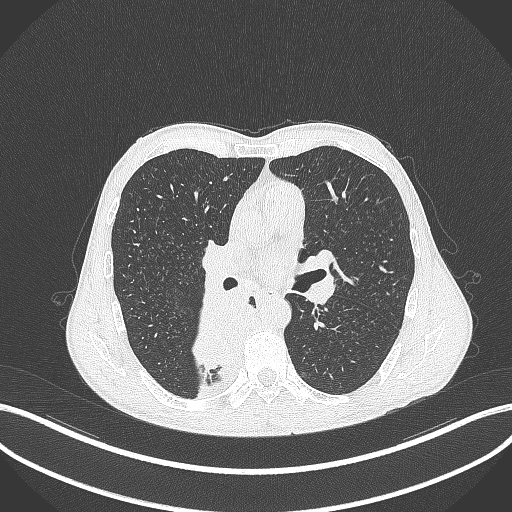
Chest CT, one axial slice. Slice 211 of 371 in the series (ordered by position). Reconstruction kernel B70f. 120 kVp. Lung window (W 1500 / L -600 HU). 512 × 512 image matrix, field of view 400 × 400 mm. Patient: male, 58 years. From the clinical record (not read from this slice): clinical TNM (as recorded): T3 N1 M1.
Outlined on this slice (rectangle marked by the reading radiologist):
- lung tumour (recorded histology: squamous cell carcinoma): bounding box (x1, y1, x2, y2) in pixels: (185, 290, 246, 377)